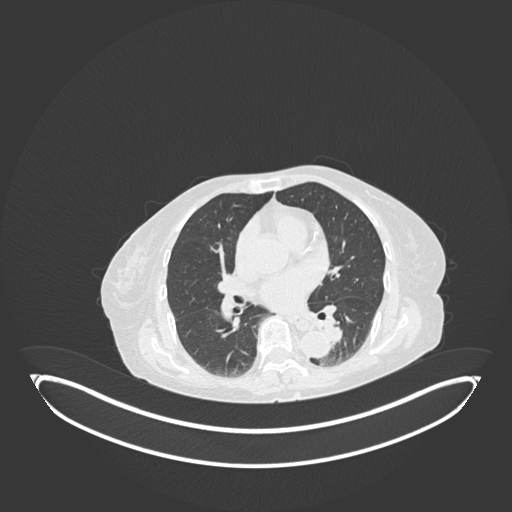
Chest CT, one axial slice; slice 60 of 189 in the series (ordered by position); 120 kVp; lung window (W 1500 / L -600 HU); 1 mm slice thickness; 512 × 512 image matrix. Female patient, age 82 years. Case-level facts recorded for this patient, not image findings: clinical TNM (as recorded): T1b N0 M1.
Annotated regions visible in this slice (bounding box drawn by a radiologist):
- lung tumour (recorded histology: adenocarcinoma): bounding box <319,318,346,350> (left, top, right, bottom; pixels)